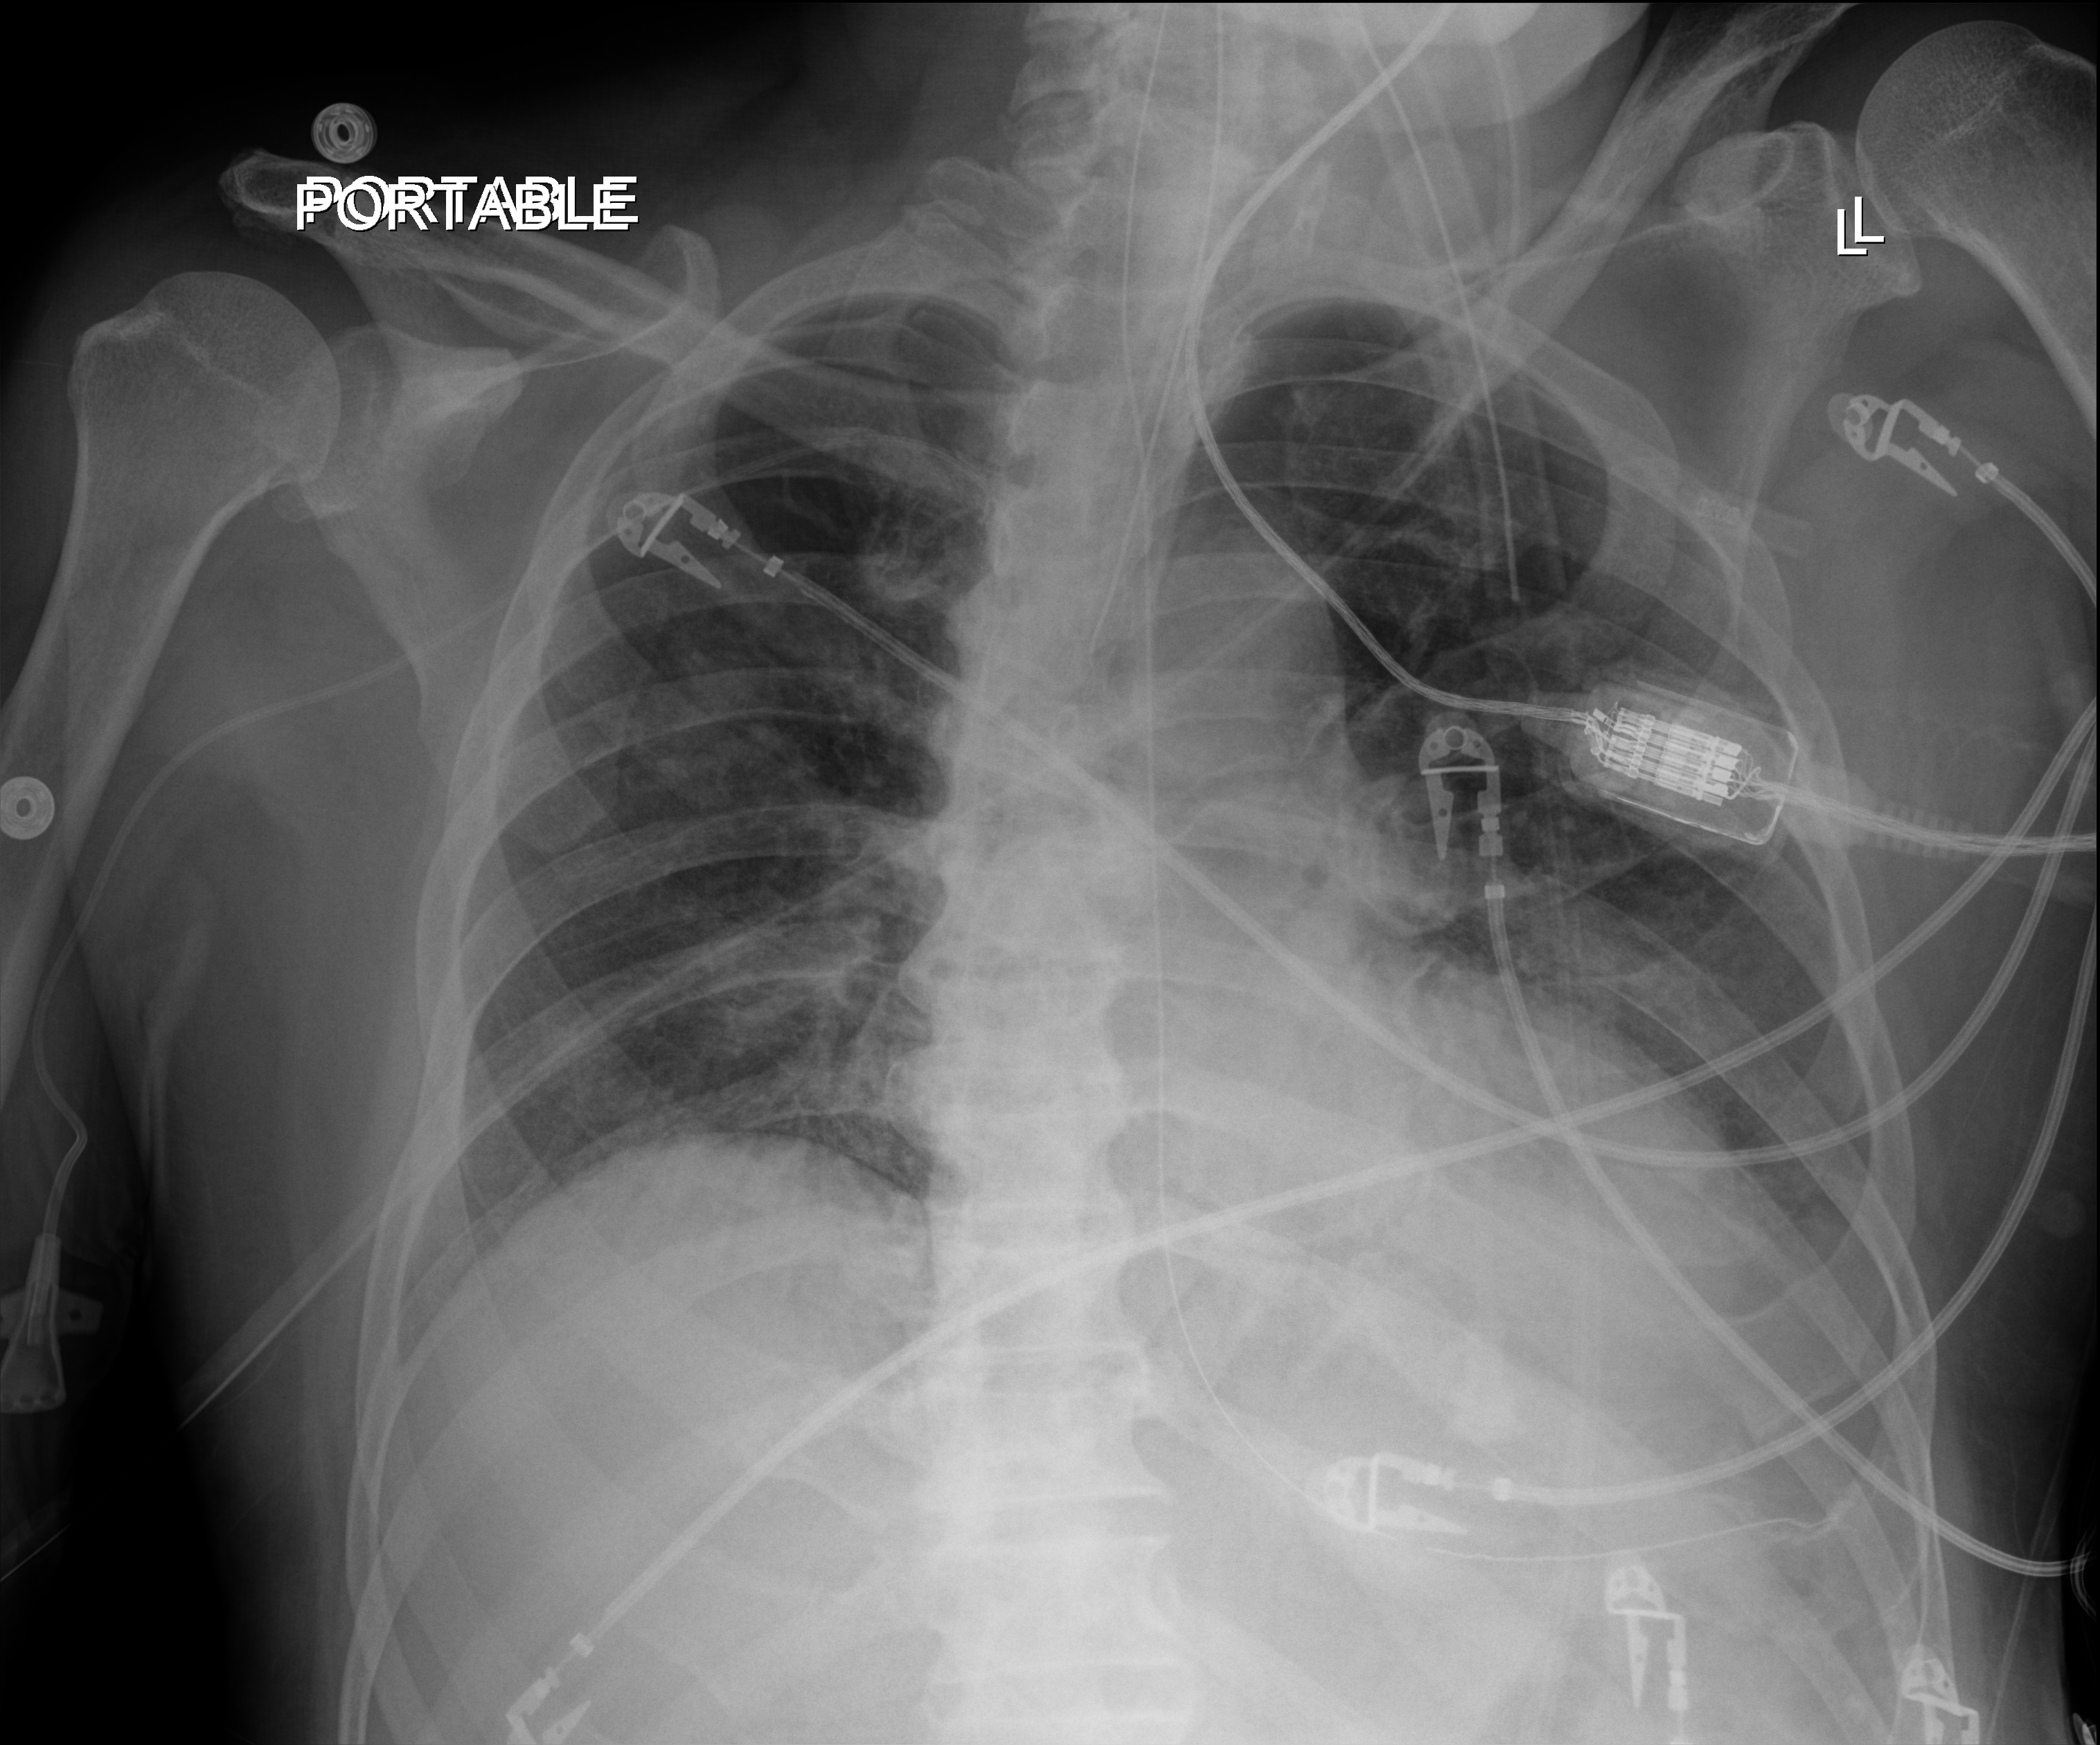
Bedside chest radiograph (digital radiography), anteroposterior (AP) projection. Male patient hospitalised with COVID-19, age 75–90 years.
Hospital-stay facts (about this admission, not read from this image; timing relative to this image not recorded):
- diabetes (admission record): no
- admitted to intensive care during this hospital stay: yes